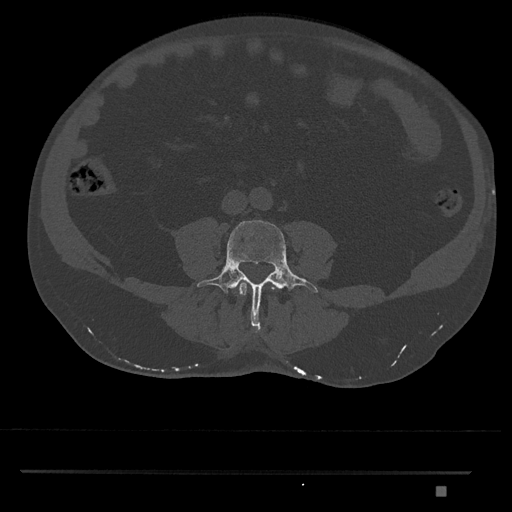
CT including the spine, one axial slice; position 625 of 1134 along the scan axis; reconstruction kernel Br40s/3; 120 kVp; bone window (W 1800 / L 400 HU); 512 × 512 image matrix, field of view 429 × 429 mm. Male patient, age 65 years. Case-level facts recorded for this patient, not image findings: primary cancer: prostate.
Annotated regions visible in this slice (semi-automatic segmentation, software-assisted and operator-edited):
- L3 vertebra: bounding box <238,282,279,296> (left, top, right, bottom; pixels)
- L4 vertebra: <197,220,318,333>